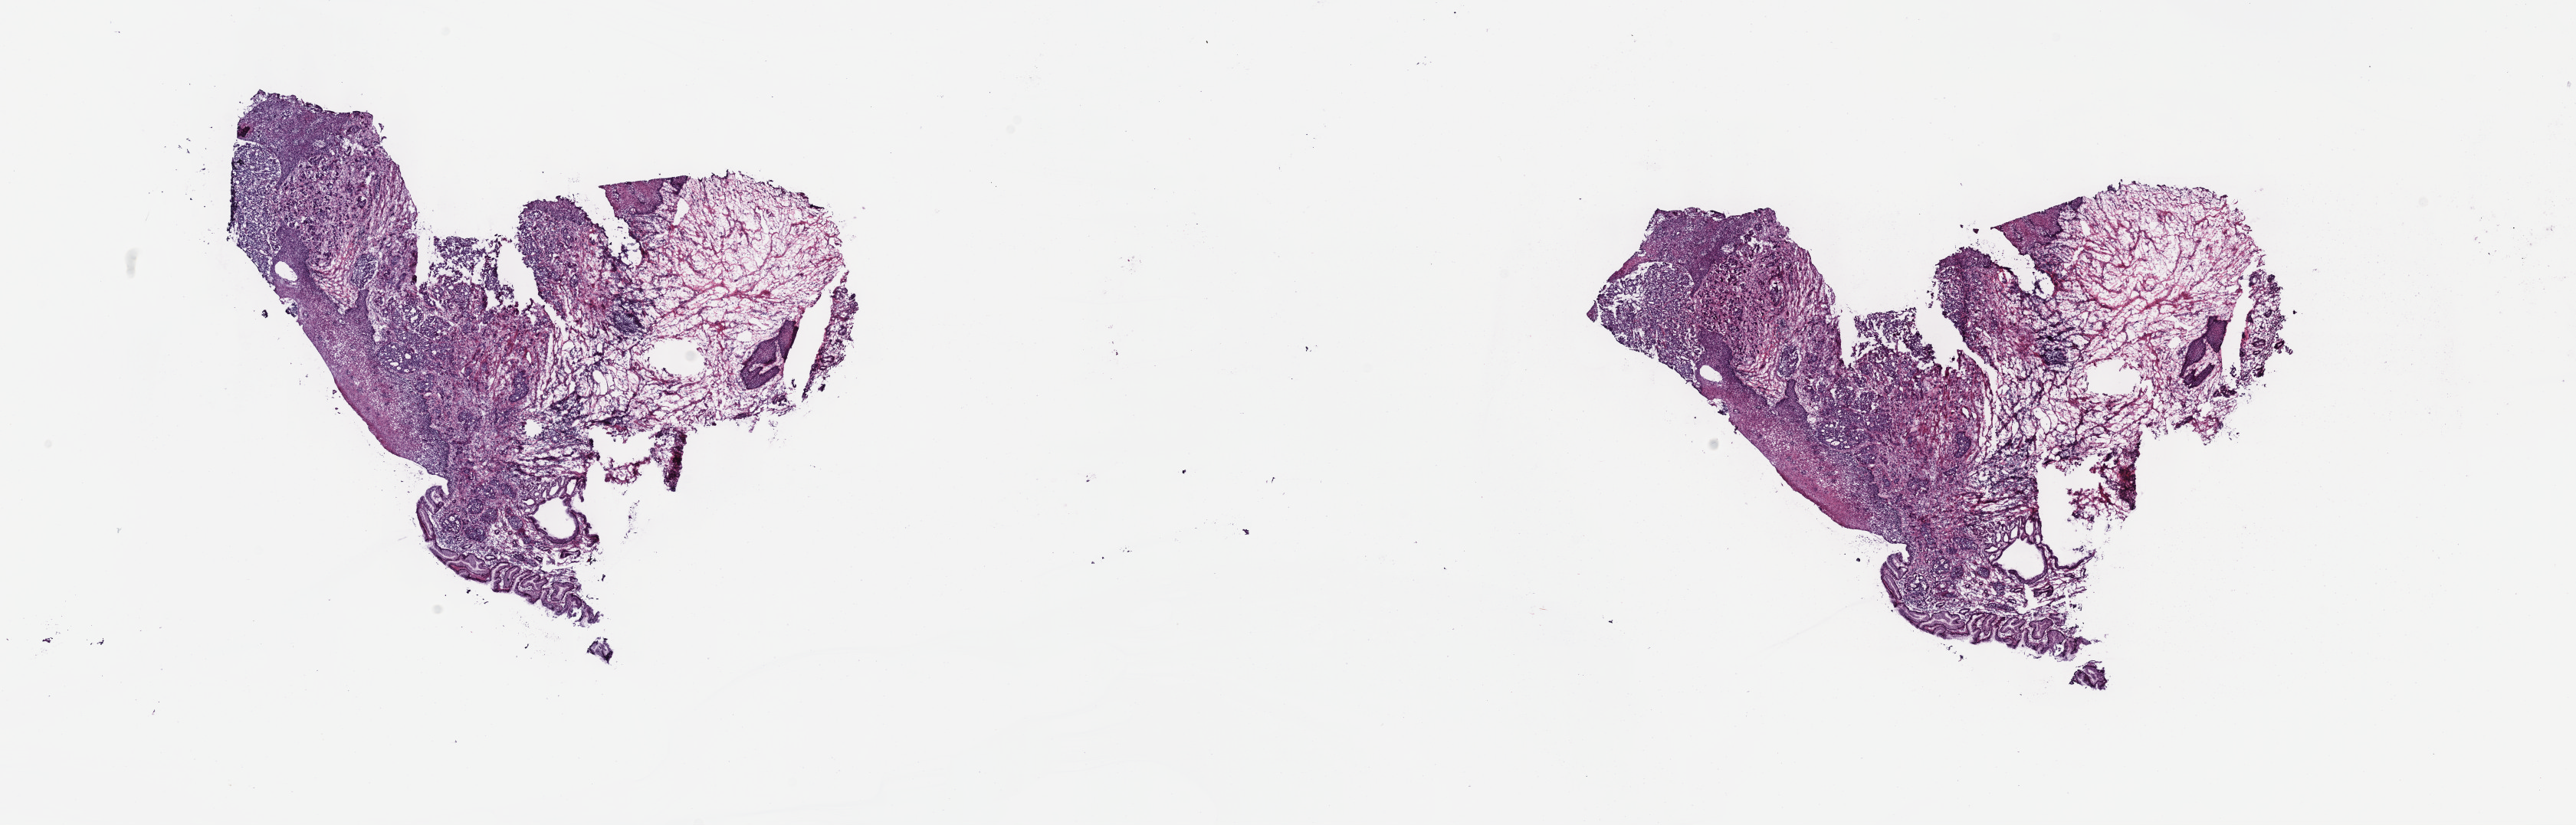
Hematoxylin and eosin (H&E) stained whole-slide image, a low-resolution overview of the entire scanned area, about 27.2 x 8.7 mm (slide scanned at 40x). Frozen section from the top of the tissue portion. Primary tumour sample from the stomach. Female patient; age at initial diagnosis 64 years. Histologic grade: G3 (poorly differentiated). Composition of this section per pathologist review: tumour cells 75%, tumour nuclei 60%, normal cells 25%, stromal cells 0%, necrosis 0%. Infiltration values recorded for this section: lymphocyte infiltration 7%, monocyte infiltration 0%, neutrophil infiltration 0%.
AJCC pathologic stage: IV (7th edition). Lymph nodes positive (case pathology): 9 of 17 examined. Diagnosis: Adenocarcinoma, NOS (cardia, NOS). TNM: T3 N3 M1.